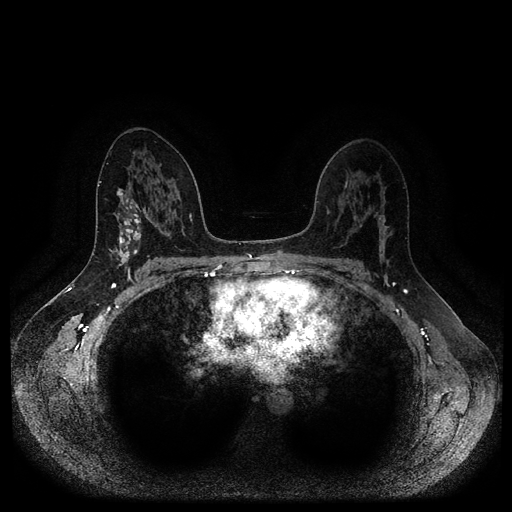
Breast MRI (dynamic contrast-enhanced, multi-phase), one axial slice. Position 60 of 116 along the scan axis. Dynamic contrast-enhanced series, time point 2 of 5 at this slice position (early post-contrast). 1.5 T. TE 2.6 ms, TR 5.3 ms. 512 × 512 image matrix. Patient: female, 45 years.
Structures marked on this image (semi-automatically segmented with operator editing):
- breast lesion (labelled benign in the annotation): bounding box [x1, y1, x2, y2] px = [115, 198, 141, 271]